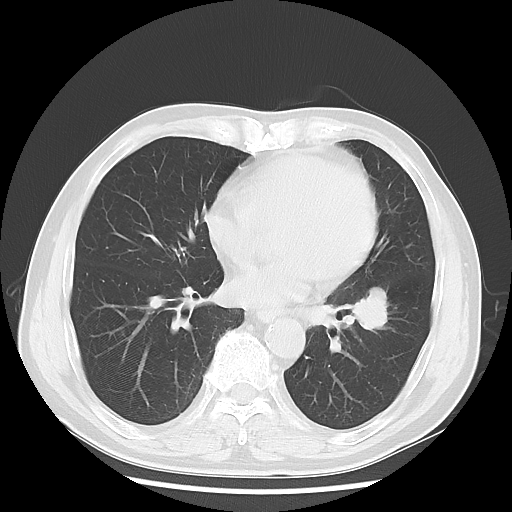
Chest CT, one axial slice. Position 28 of 68 along the scan axis. Reconstruction kernel LUNG. 120 kVp. Lung window (W 1500 / L -600 HU). 5 mm slice thickness. 512 × 512 image matrix, field of view 360 × 360 mm. Patient: male, 71 years. Case-level facts recorded for this patient, not image findings: clinical TNM (as recorded): T1c N1 M0.
Annotated regions visible in this slice (rectangle marked by the reading radiologist):
- lung tumour (recorded histology: adenocarcinoma): bounding box <348,285,393,337> (left, top, right, bottom; pixels)